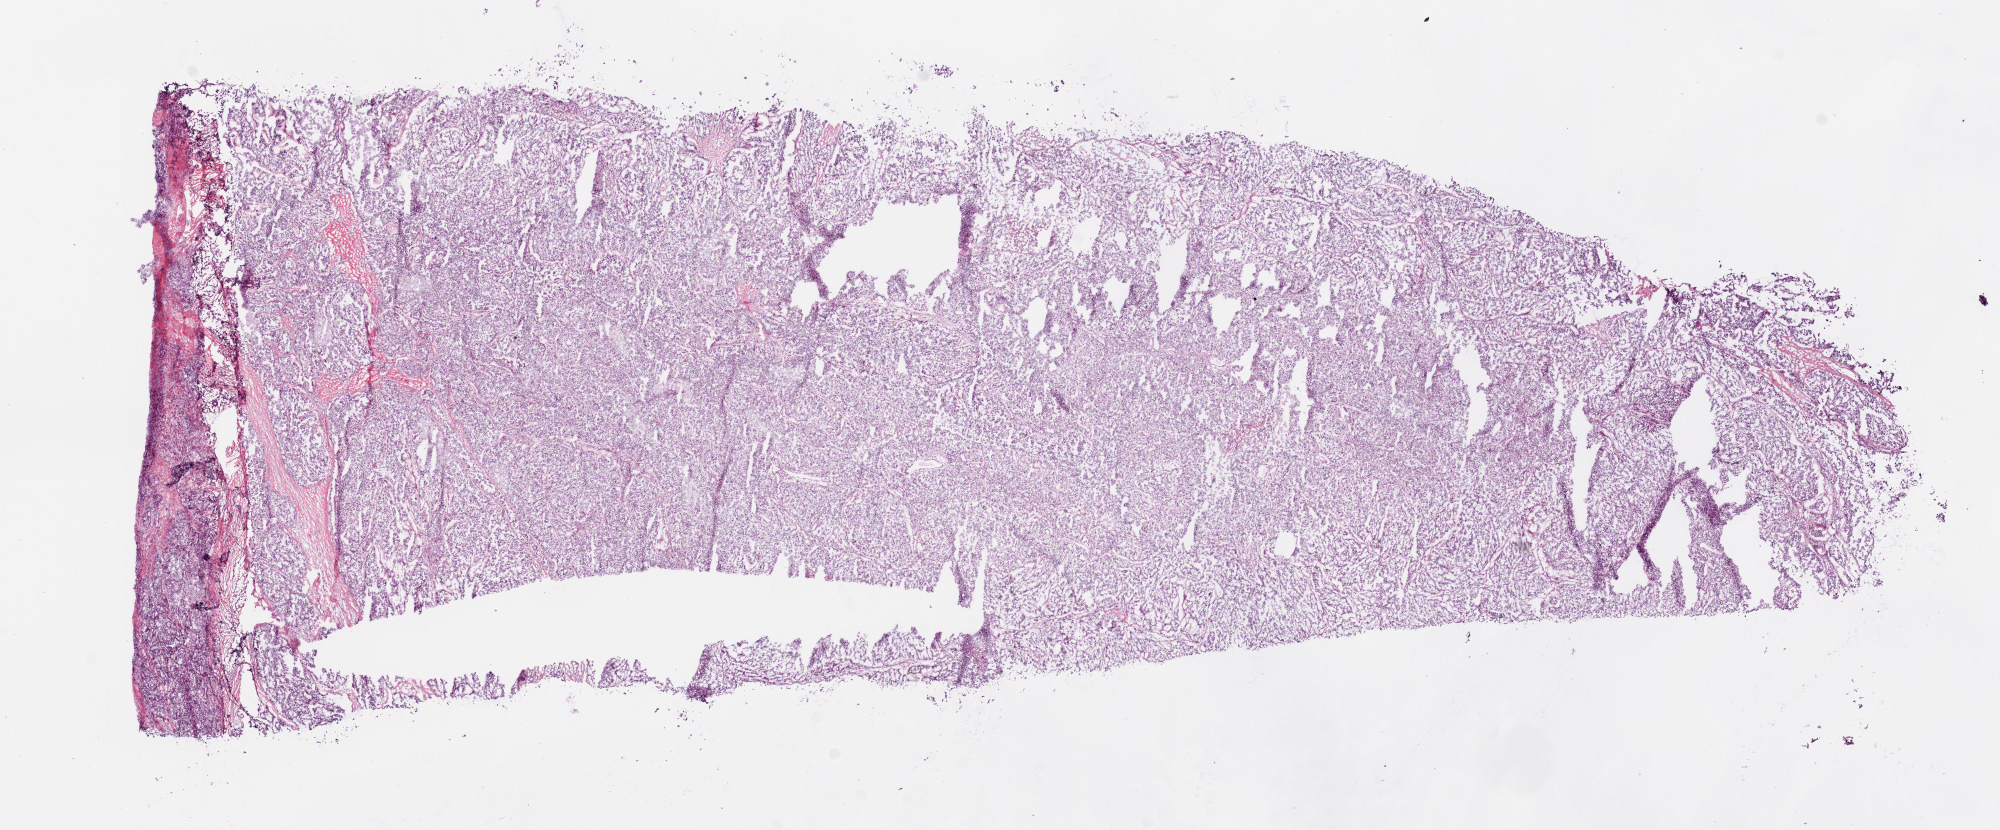
H&E whole-slide image, whole scanned area (about 16.0 x 6.7 mm, acquisition: 20x scan) shown as a low-resolution overview; frozen section from the top of the tissue portion; kidney, primary tumour sample. Male patient; age at initial diagnosis 33 years. Histologic grade: G3 (poorly differentiated). Composition of this section per pathologist review: tumour cells 90%, tumour nuclei 85%, normal cells 0%, stromal cells 10%, necrosis 0%.
- TNM: T3a N1 M1
- AJCC pathologic stage: IV
- histologic diagnosis: Clear cell adenocarcinoma, NOS
- lymph nodes positive (case pathology): 1 of 1 examined